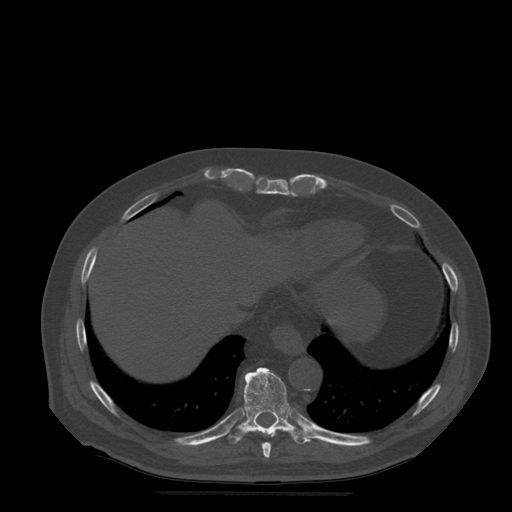
CT including the spine, one axial slice; position 274 of 522 along the scan axis; bone window (W 1800 / L 400 HU); 1.25 mm slice thickness; 512 × 512 image matrix. Patient age 72 years. Case-level facts recorded for this patient, not image findings: primary cancer: prostate.
Outlined on this slice (semi-automatic segmentation, software-assisted and operator-edited):
- T10 vertebra: bounding box <228,368,315,444> (left, top, right, bottom; pixels)
- T9 vertebra: <262,443,272,459>